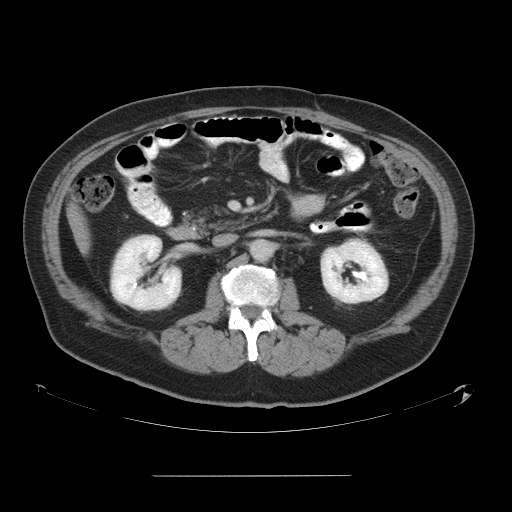
Contrast-enhanced abdominal CT, one axial slice. Slice 19 of 58 in the series (ordered by position). Intravenous contrast given. Soft-tissue window (W 400 / L 40 HU). 512 × 512 image matrix, field of view 480 × 480 mm. Male patient, age 63 years. From the clinical record (not read from this slice): diagnosis: colorectal cancer liver metastases, imaged before liver resection; multiple liver metastases: no; largest metastasis: 4.2 cm.
Structures marked on this image (expert manual segmentation):
- liver: bounding box <76,220,87,245> (left, top, right, bottom; pixels)
- planned liver remnant (the part of the liver to remain after resection): <75,215,86,241>